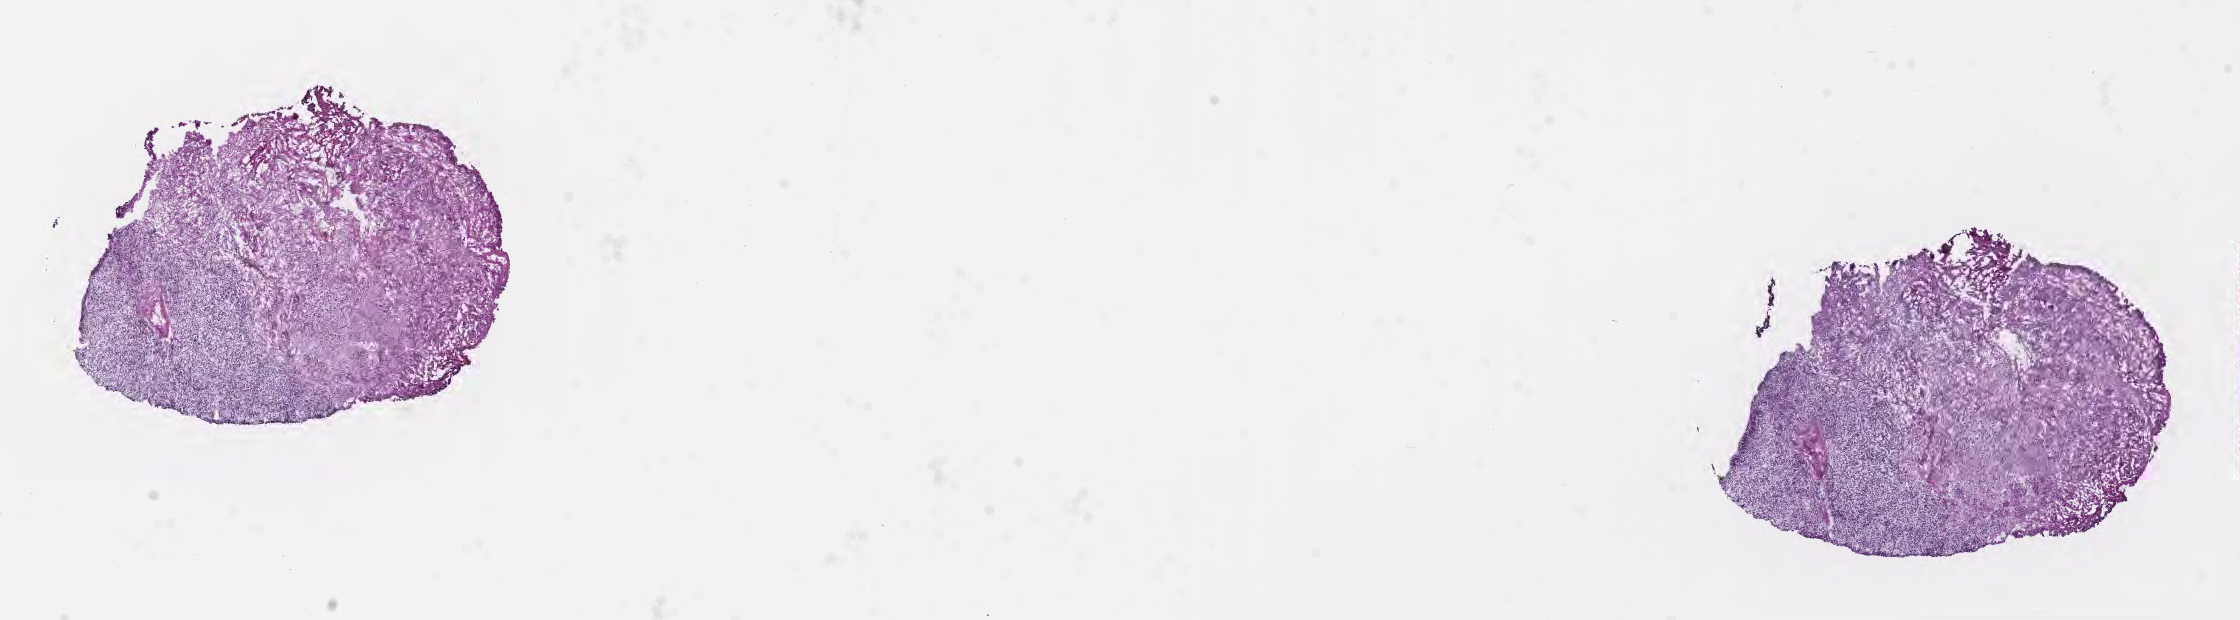
Haematoxylin and eosin whole-slide image, a low-resolution overview of the entire scanned area, about 18.1 x 5.0 mm. Frozen section (tissue freezing medium). Specimen: primary tumor. Site: brain. Female patient; age at initial diagnosis 49 years. Composition of this section per pathologist review: tumor cells 87%, tumor nuclei 93%, stromal cells 6%, necrosis 0%, normal cells 7%. Infiltration values recorded for this section: lymphocyte infiltration 0%, monocyte infiltration 0%, neutrophil infiltration 0%.
Section: bottom of the tissue portion. Diagnosis: Glioblastoma, NOS.